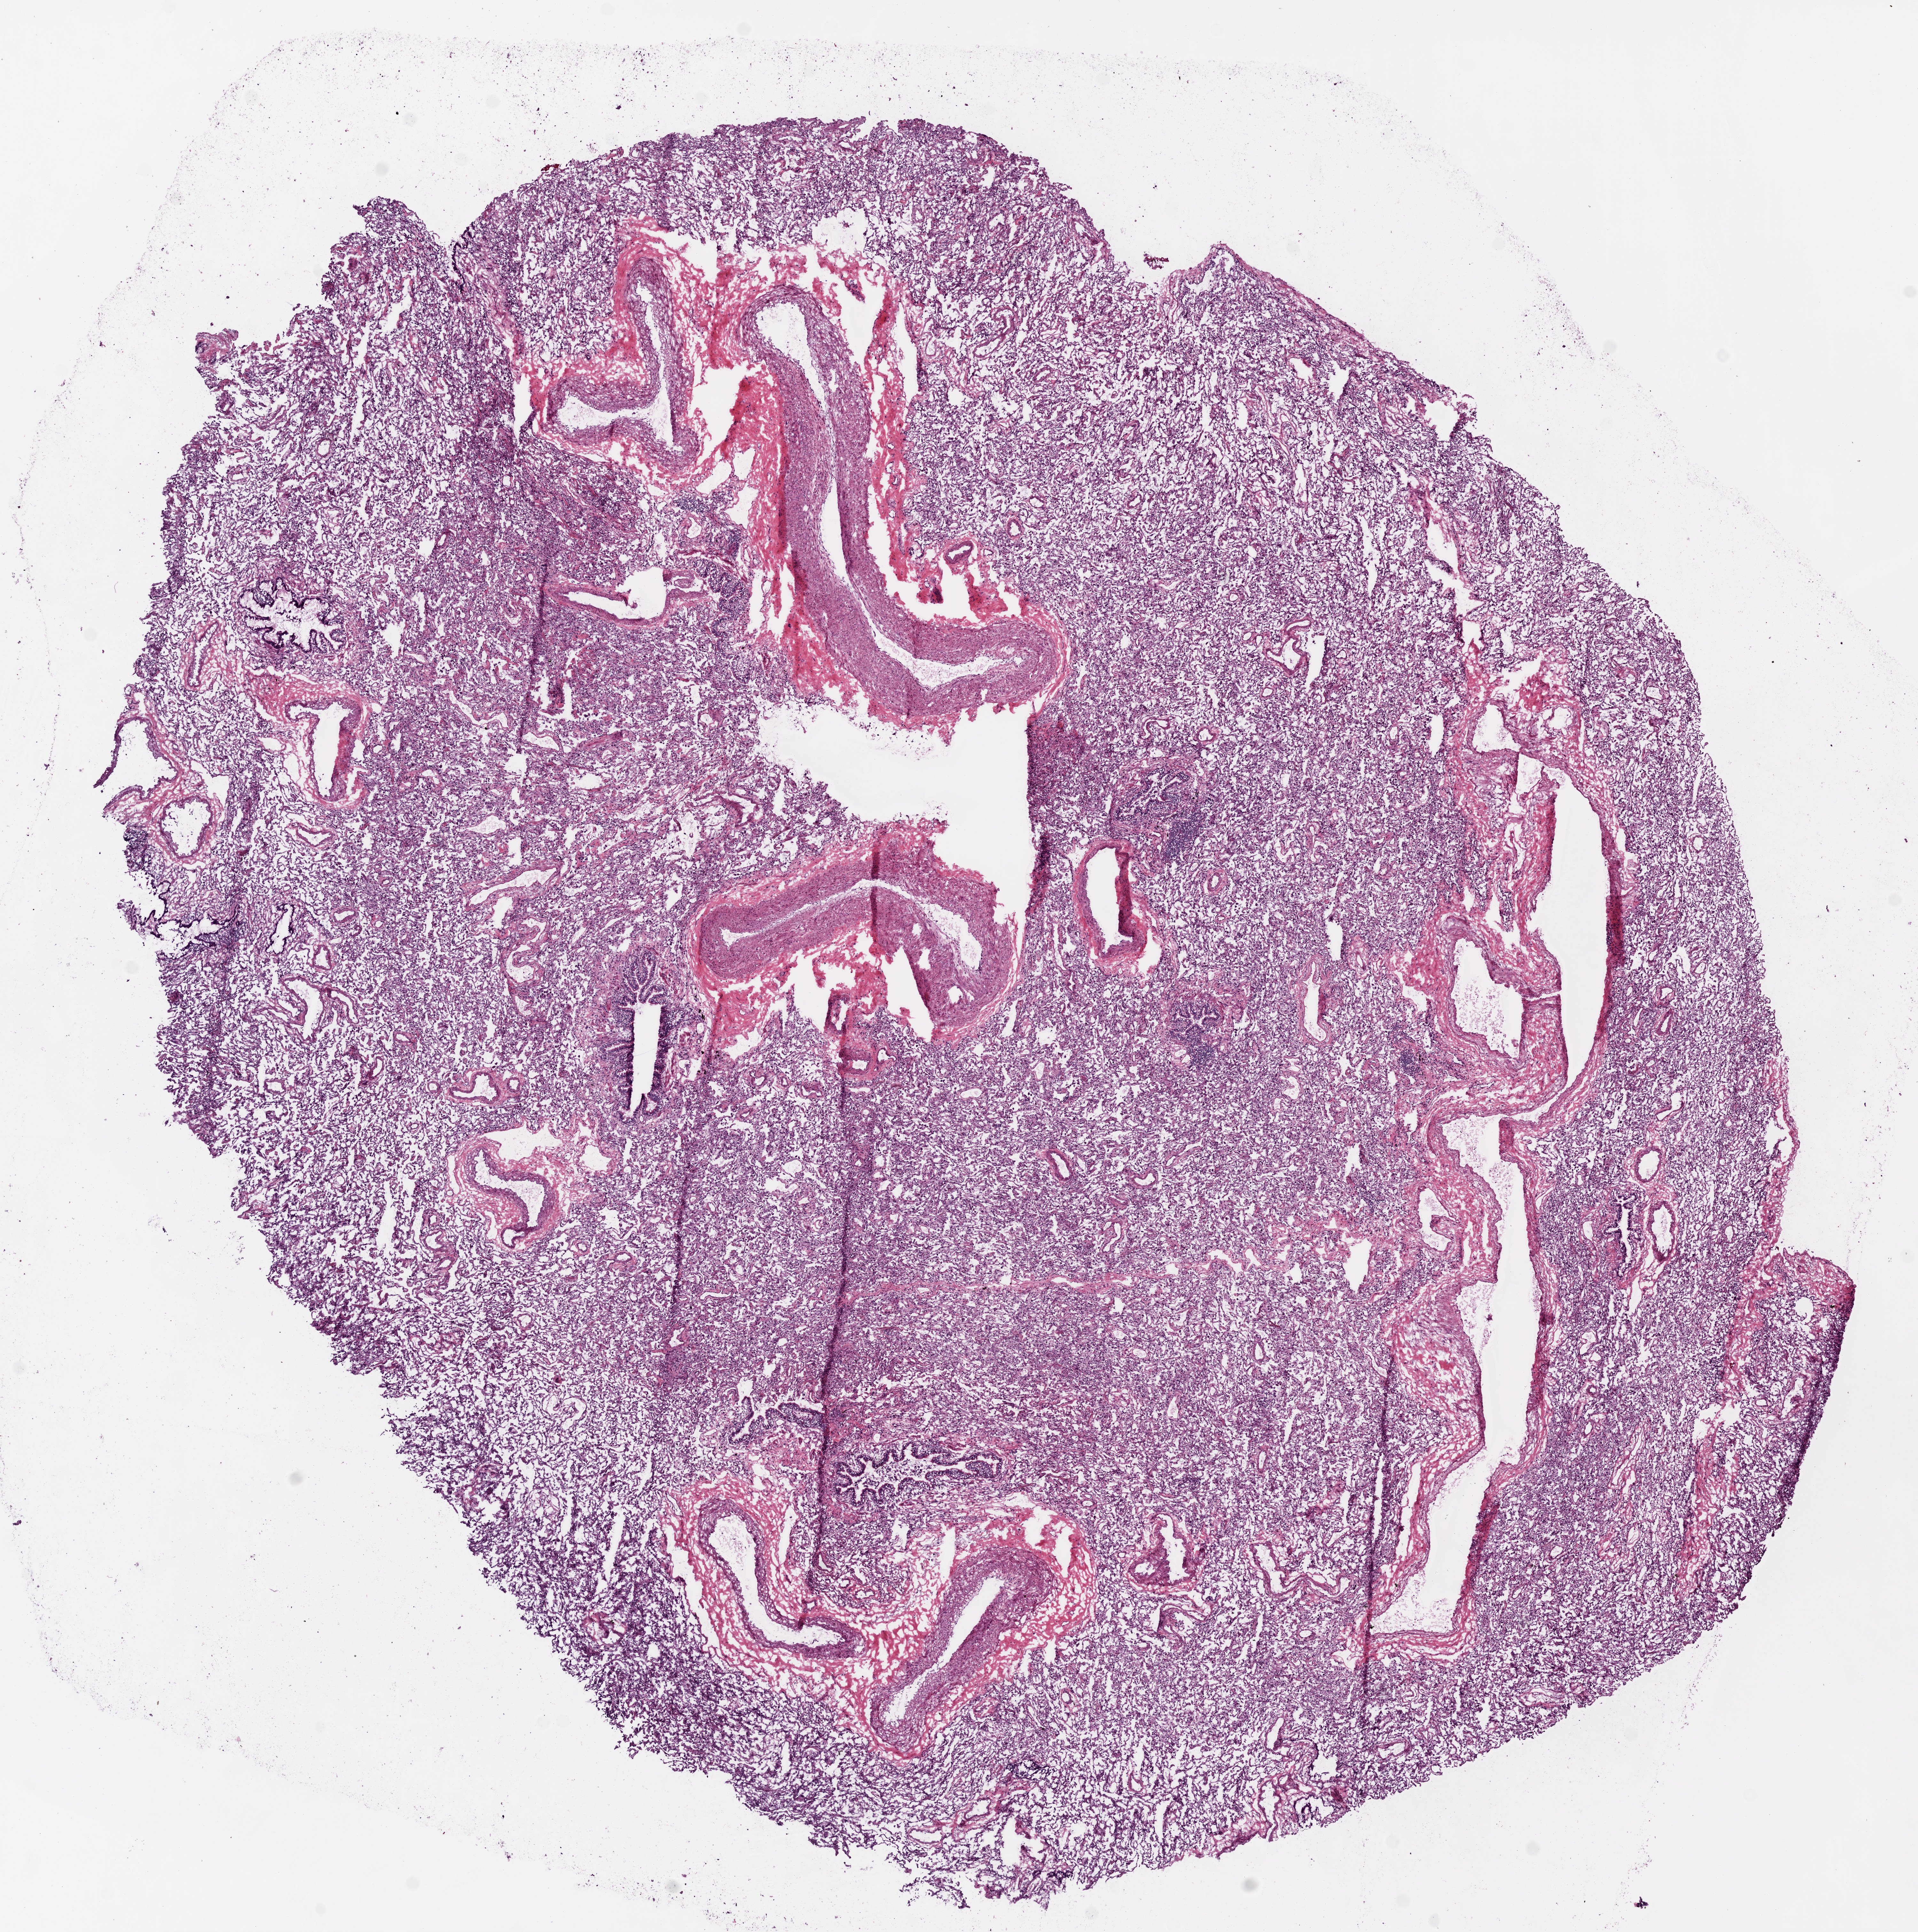
Whole-slide histology image, H&E, shown as a low-resolution overview of the whole scanned area (about 12.0 x 12.1 mm); frozen section from the bottom of the tissue portion; sample: solid tissue normal (non-tumour tissue), lung. Female, age 61 years at initial diagnosis.
This section: solid tissue normal (non-tumour) sample from the same patient. Patient diagnosis: Adenocarcinoma, NOS.